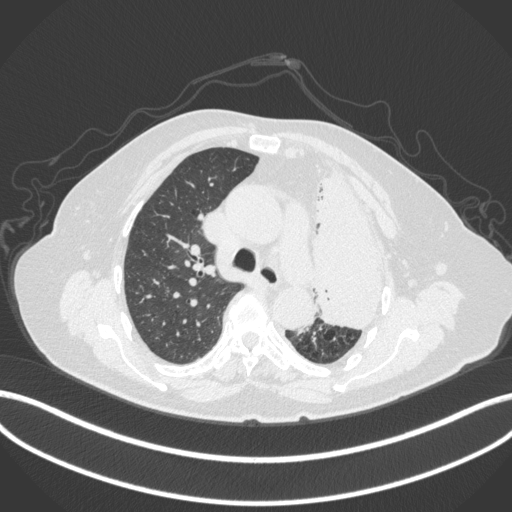
Chest CT, one axial slice. Slice 270 of 399 in the series (ordered by position). Reconstruction kernel B31f. 120 kVp. Lung window (W 1500 / L -600 HU). 1 mm slice thickness. 512 × 512 image matrix. Patient: female, 75 years. From the clinical record (not read from this slice): clinical TNM (as recorded): T3 N3 M1.
Outlined on this slice (bounding box drawn by a radiologist):
- lung tumour (recorded histology: adenocarcinoma): bounding box (x1, y1, x2, y2) in pixels: (305, 156, 401, 339)